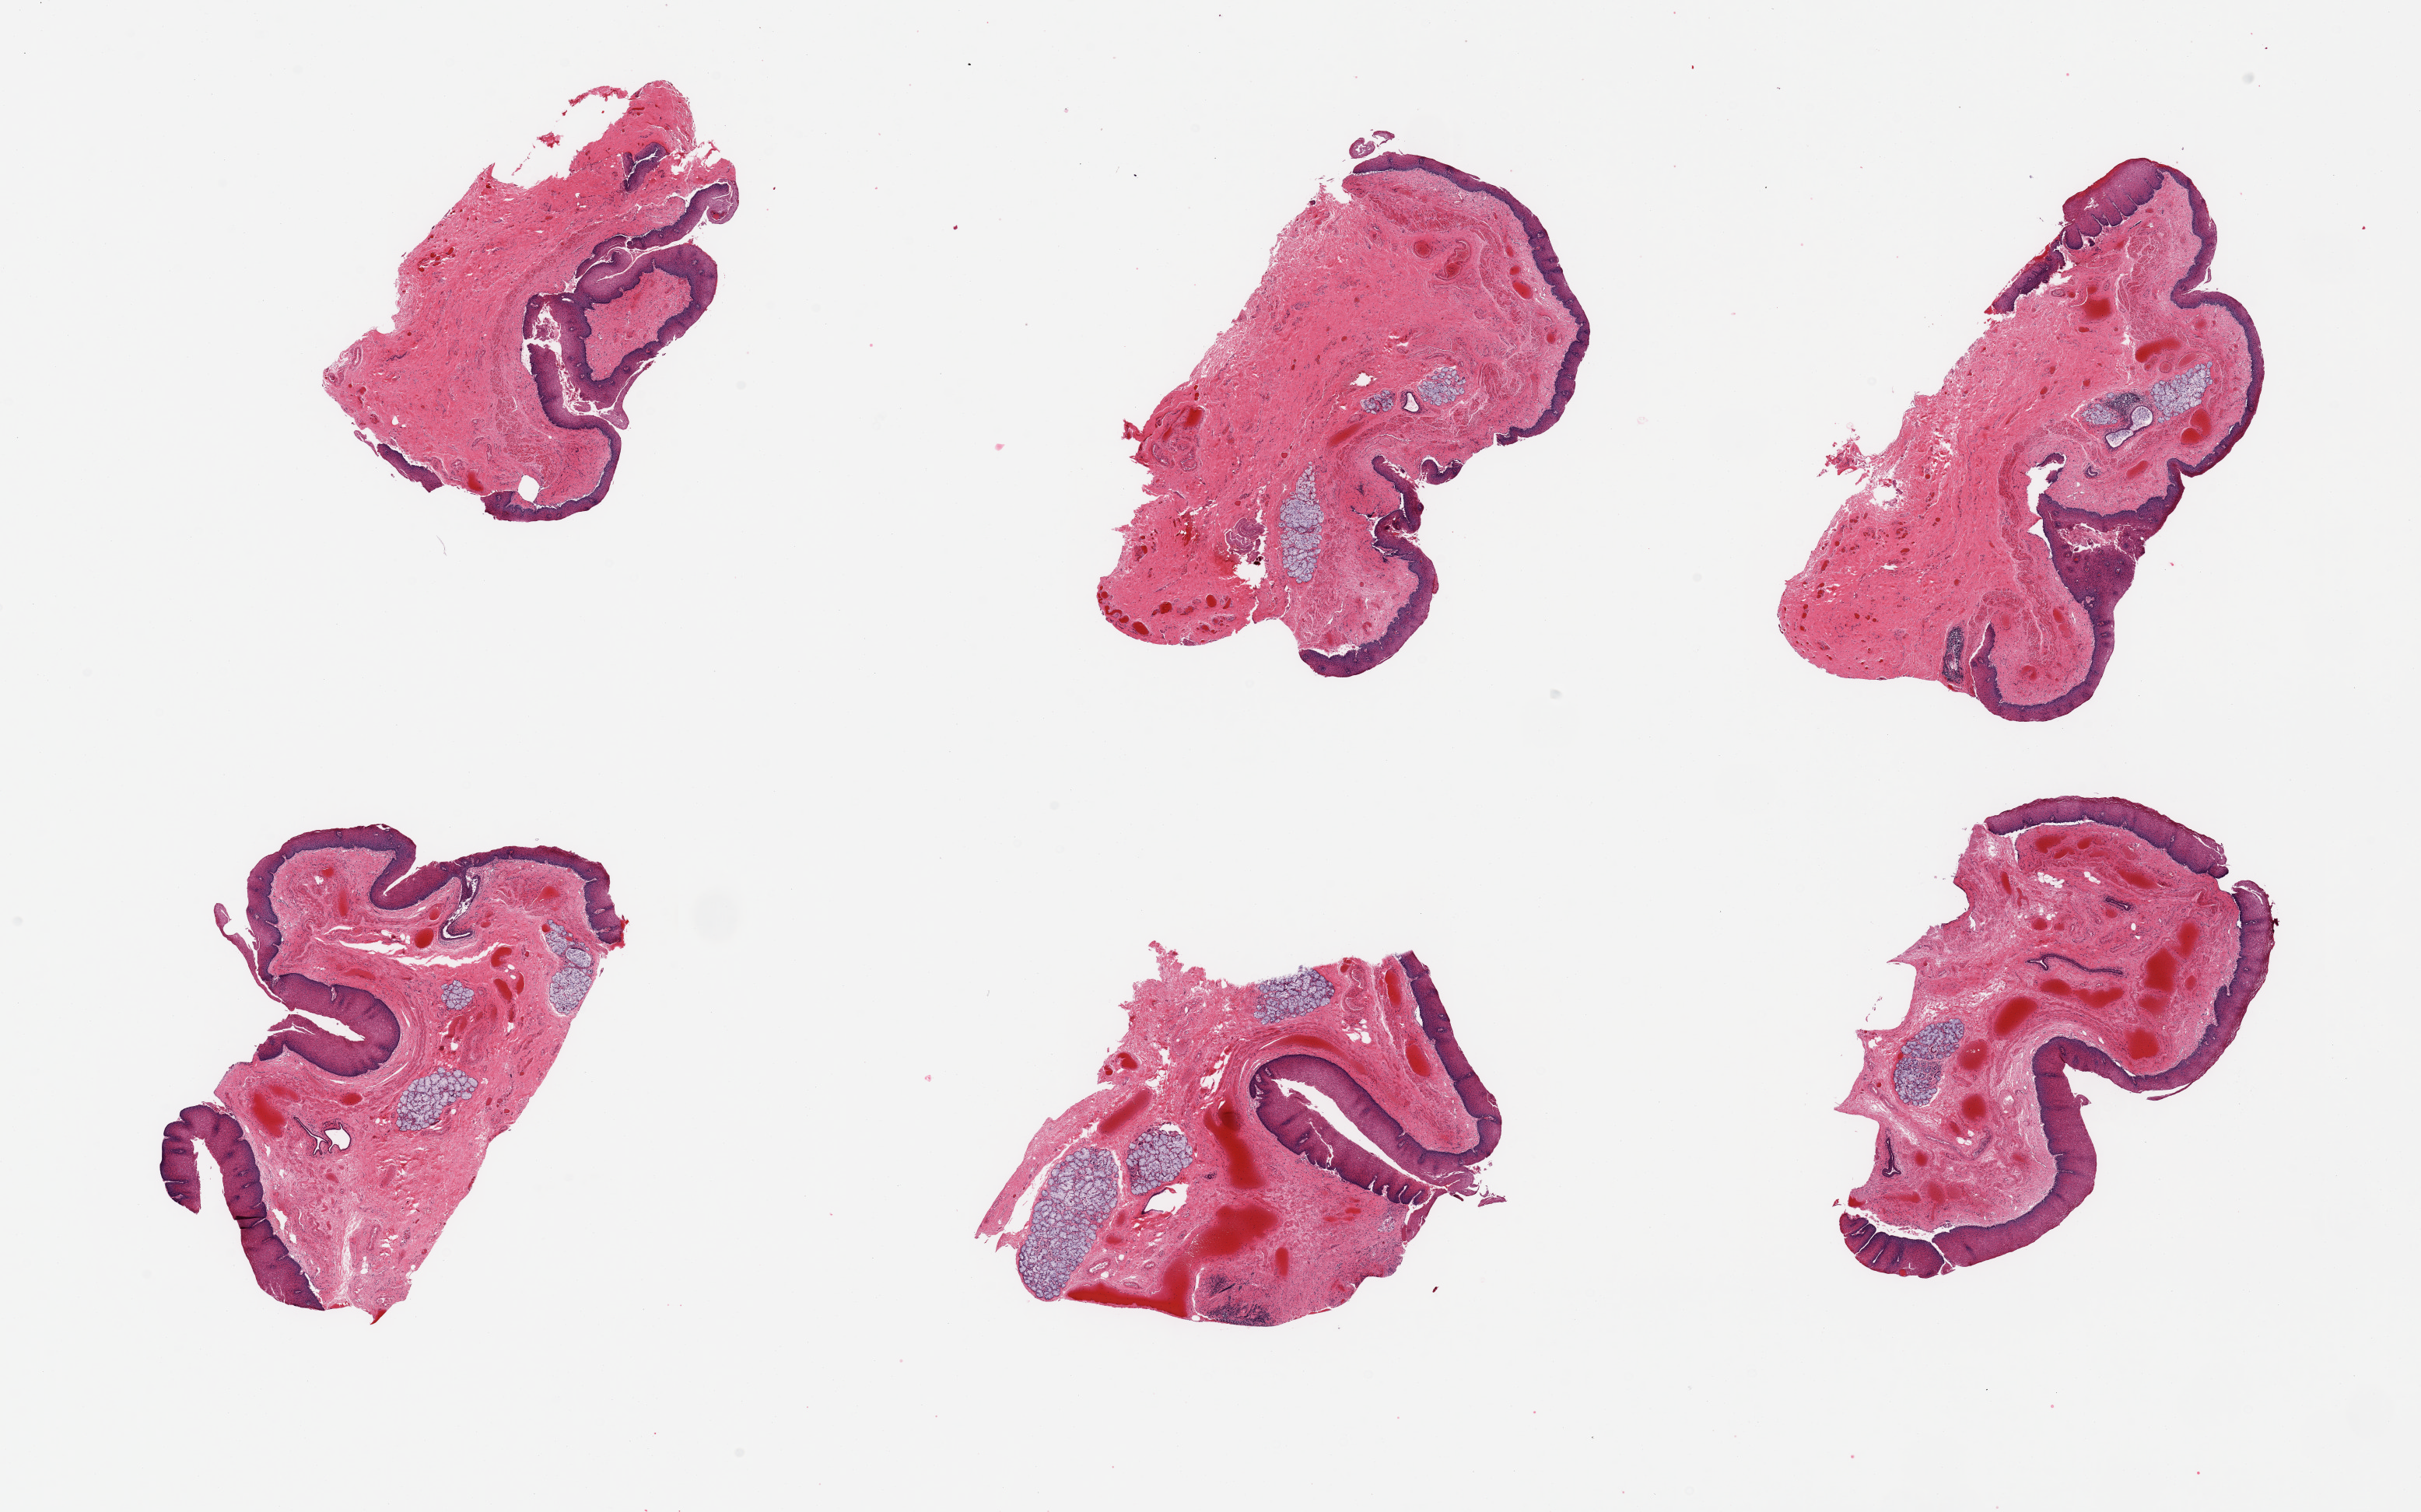
H&E whole-slide image, shown as a low-resolution overview of the whole scanned area (about 24.6 x 15.4 mm, slide scanned at 20x); PAXgene-fixed, paraffin-embedded tissue; section of esophageal mucous membrane (target tissue); tissue donor sample. Donor sex: male.
* reviewer comment on this tissue sample: 6 pieces; congestion, includes several clusters of submucosal glands